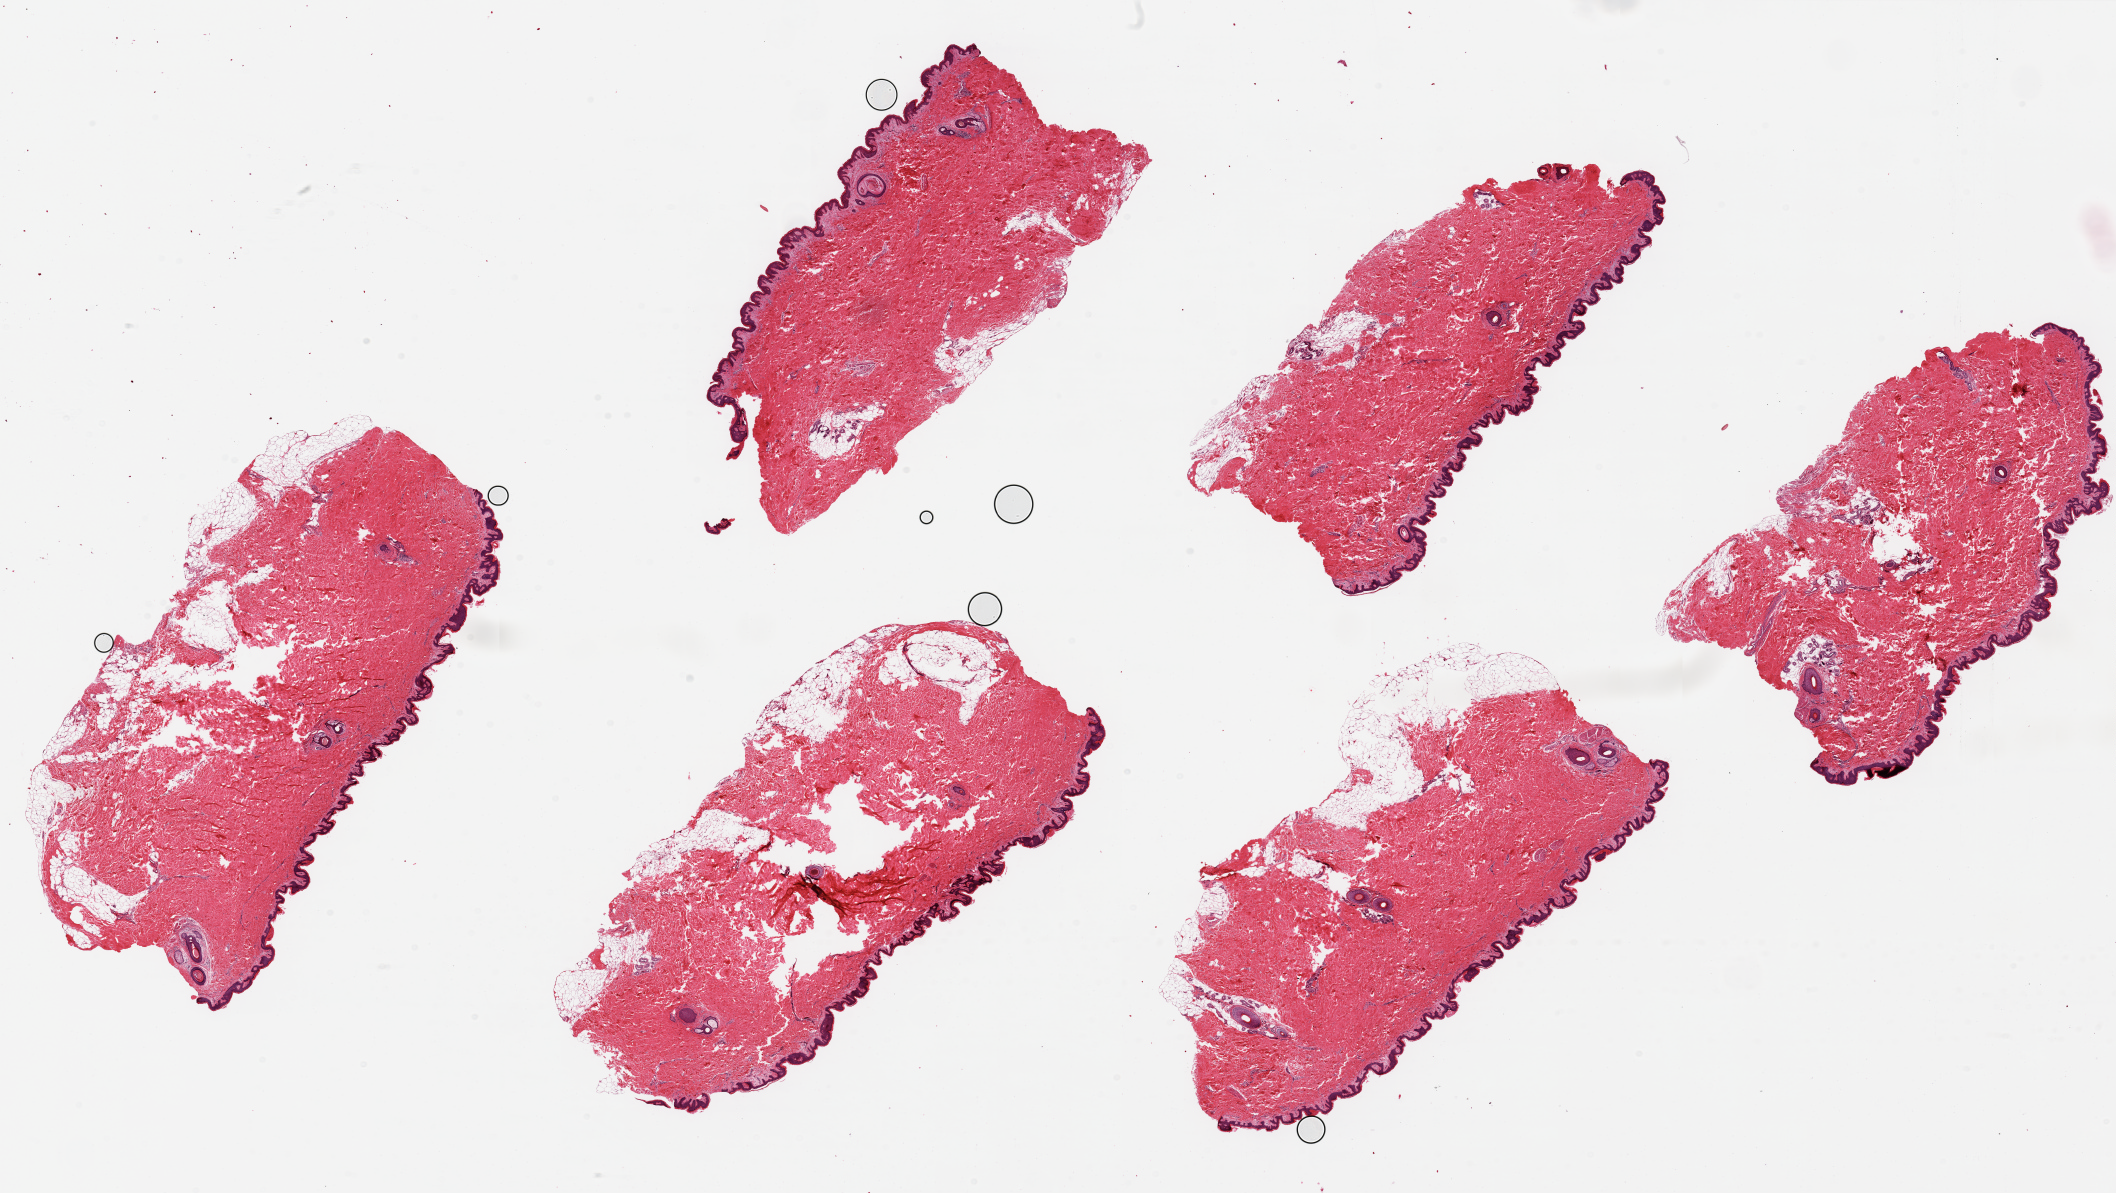
Digitized haematoxylin and eosin-stained section — whole scanned area (about 33.5 x 18.9 mm) shown as a low-resolution overview; PAXgene-fixed paraffin-embedded (PFPE) section; section of skin of suprapubic region (target tissue); donor tissue sample. Donor sex: male.
• reviewer comment on this tissue sample: 6 pieces up to ~9x4.5mm; squamous epithelium is is ~1% of thickness